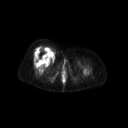
FDG PET of an extremity soft-tissue mass (from a PET/CT study), one axial slice; position 53 of 267 along the scan axis; 128 × 128 image matrix. Patient: female, 56 years. From the clinical record (not read from this slice): histological type: malignant solitary fibrous tumor; grade: intermediate; site of the primary tumour: right thigh.
Annotated regions visible in this slice (expert contour drawn on MRI and transferred to this co-registered scan by the dataset authors):
- gross tumour volume including surrounding oedema: box from (x=32, y=46) to (x=54, y=62) px
- gross tumour volume (mass): (x=32, y=46)–(x=53, y=62)